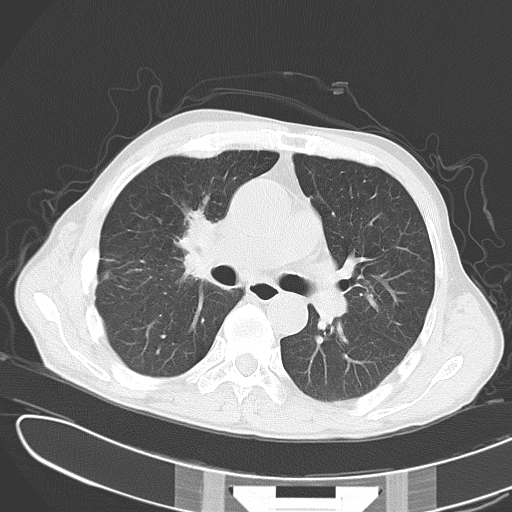
Chest CT, one axial slice. Slice 21 of 43 in the series (ordered by position). Reconstruction kernel B70f. 120 kVp. Lung window (W 1500 / L -600 HU). 5 mm slice thickness. 512 × 512 image matrix. Male patient, age 65 years. From the clinical record (not read from this slice): clinical TNM (as recorded): T2 N3 M1.
Structures marked on this image (rectangle marked by the reading radiologist):
- lung tumour (recorded histology: small cell carcinoma): bounding box (x1, y1, x2, y2) in pixels: (175, 196, 225, 298)